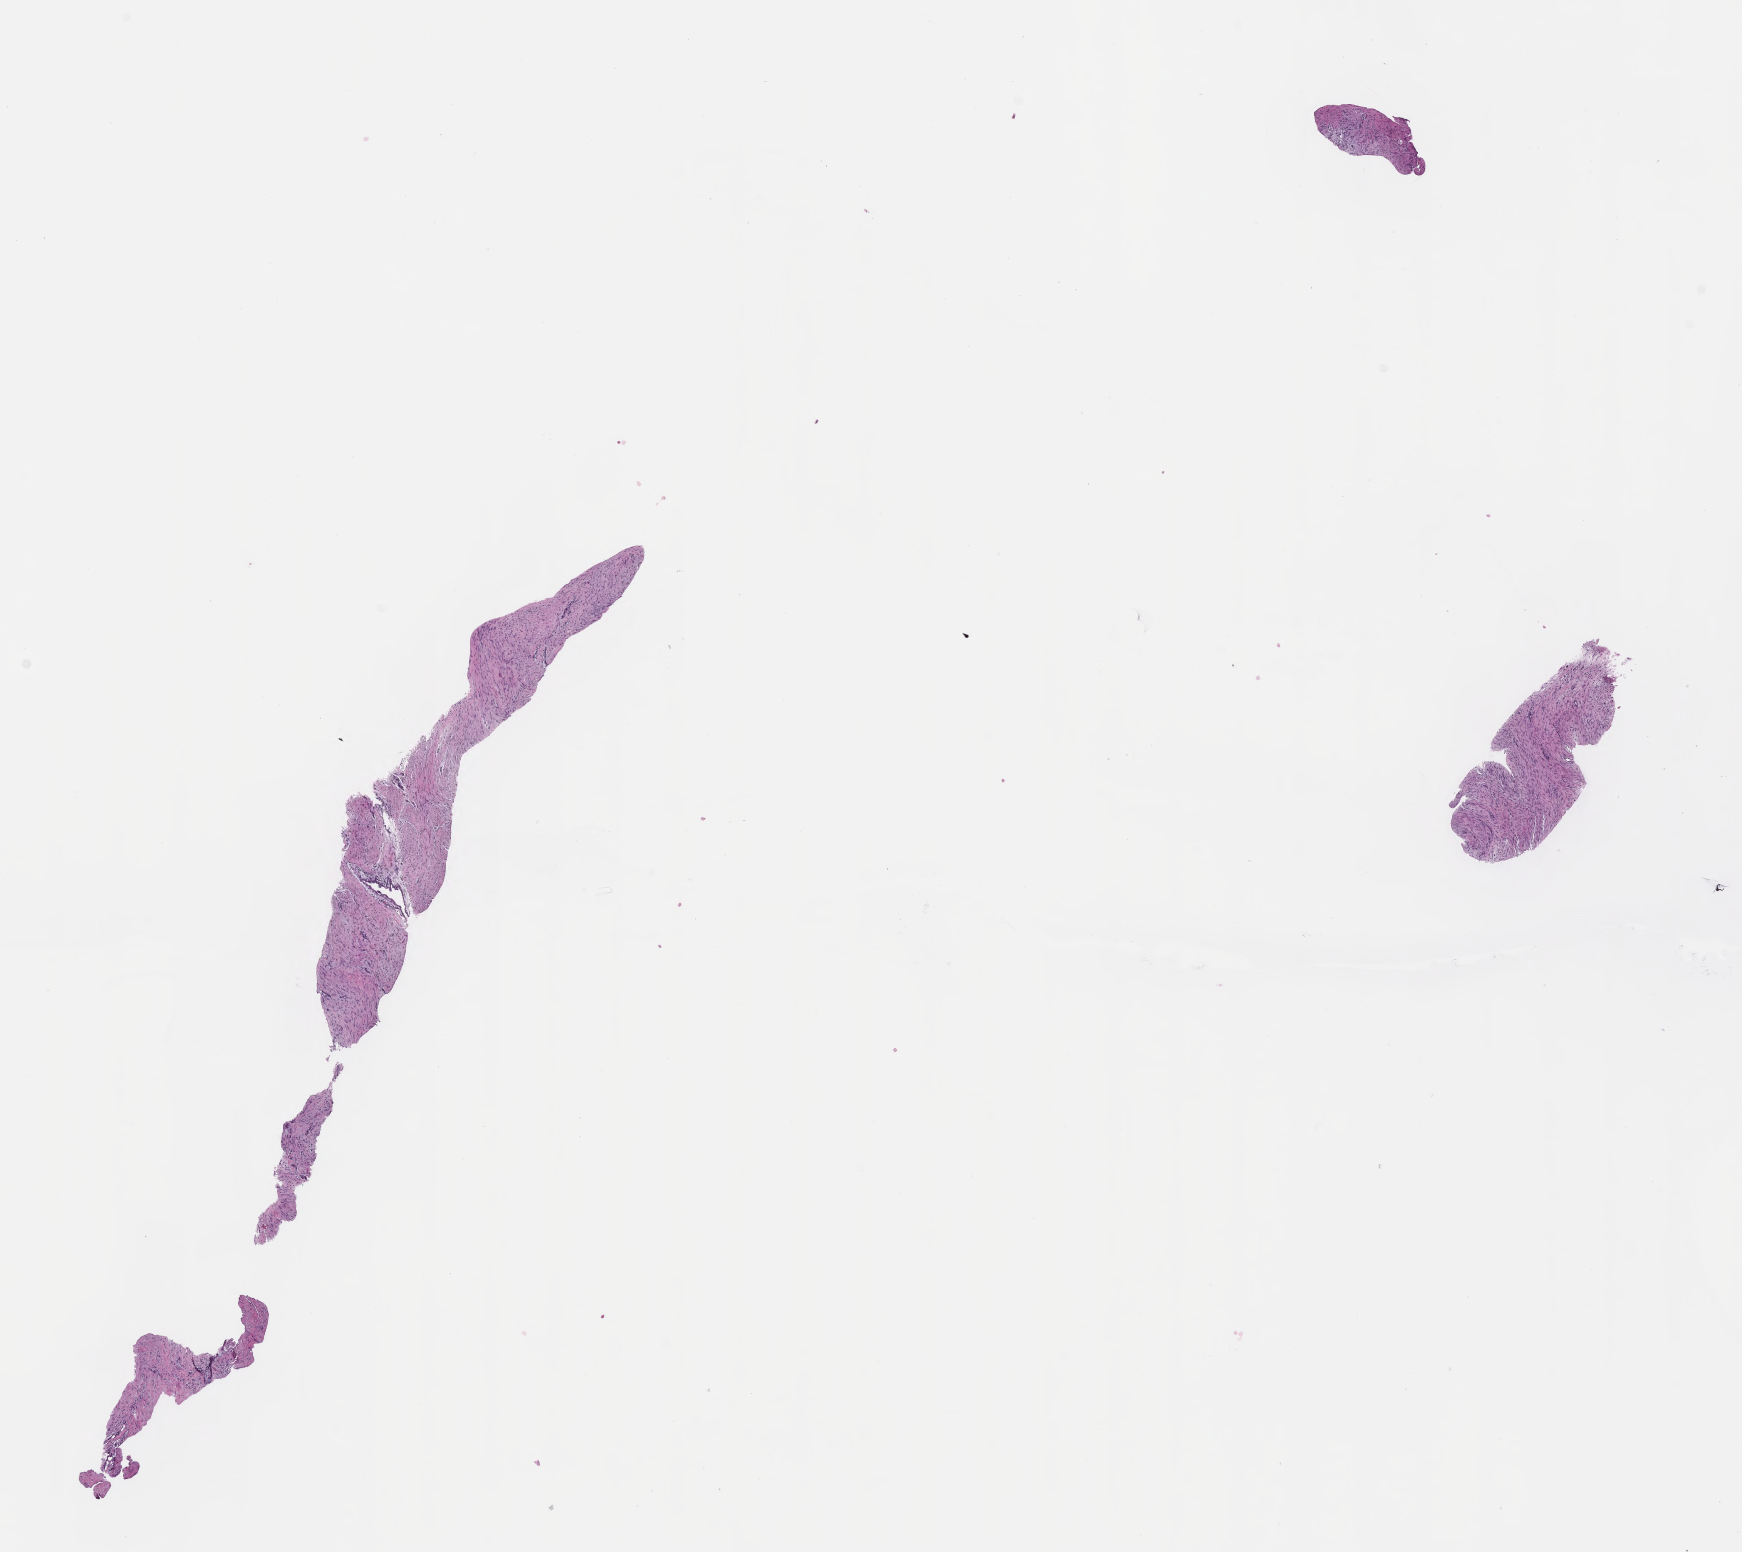
Whole-slide image, H&E stain of tumor tissue from the upper limb lymph node — low-resolution overview of the scanned area, about 14.1 x 12.6 mm; formalin-fixed paraffin-embedded section. Patient male; age 260 months (21 years 8 months).
Recorded diagnosis: Aggressive fibromatosis.